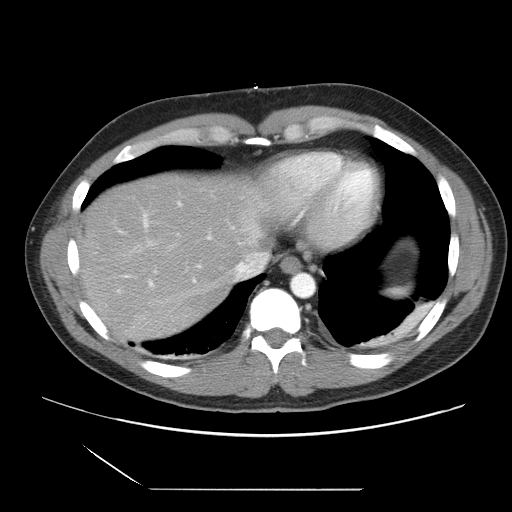
Contrast-enhanced abdominal CT, one axial slice; slice 28 of 39 in the series (ordered by position); 120 kVp; intravenous contrast given; soft-tissue window (W 400 / L 40 HU); 5 mm slice thickness; 512 × 512 image matrix, field of view 395 × 395 mm. Male patient, age 39 years. Case-level facts recorded for this patient, not image findings: diagnosis: colorectal cancer liver metastases, imaged before liver resection; multiple liver metastases: yes.
Annotated regions visible in this slice (manually delineated by an expert):
- hepatic veins: bounding box (x1, y1, x2, y2) in pixels: (163, 253, 258, 308)
- liver: (78, 176, 271, 343)
- planned liver remnant (the part of the liver to remain after resection): (135, 176, 272, 253)
- portal vein (with intrahepatic branches): (121, 202, 195, 289)